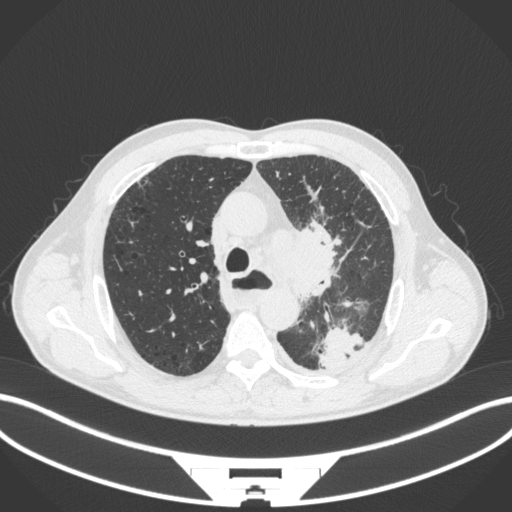
Chest CT, one axial slice. Slice 271 of 411 in the series (ordered by position). 120 kVp. Lung window (W 1500 / L -600 HU). 1 mm slice thickness. 512 × 512 image matrix, field of view 400 × 400 mm. Male patient, age 57 years. Case-level facts recorded for this patient, not image findings: clinical TNM (as recorded): T2a N1 M0.
Structures marked on this image (rectangle marked by the reading radiologist):
- lung tumour (recorded histology: squamous cell carcinoma): box from (x=269, y=225) to (x=349, y=300) px